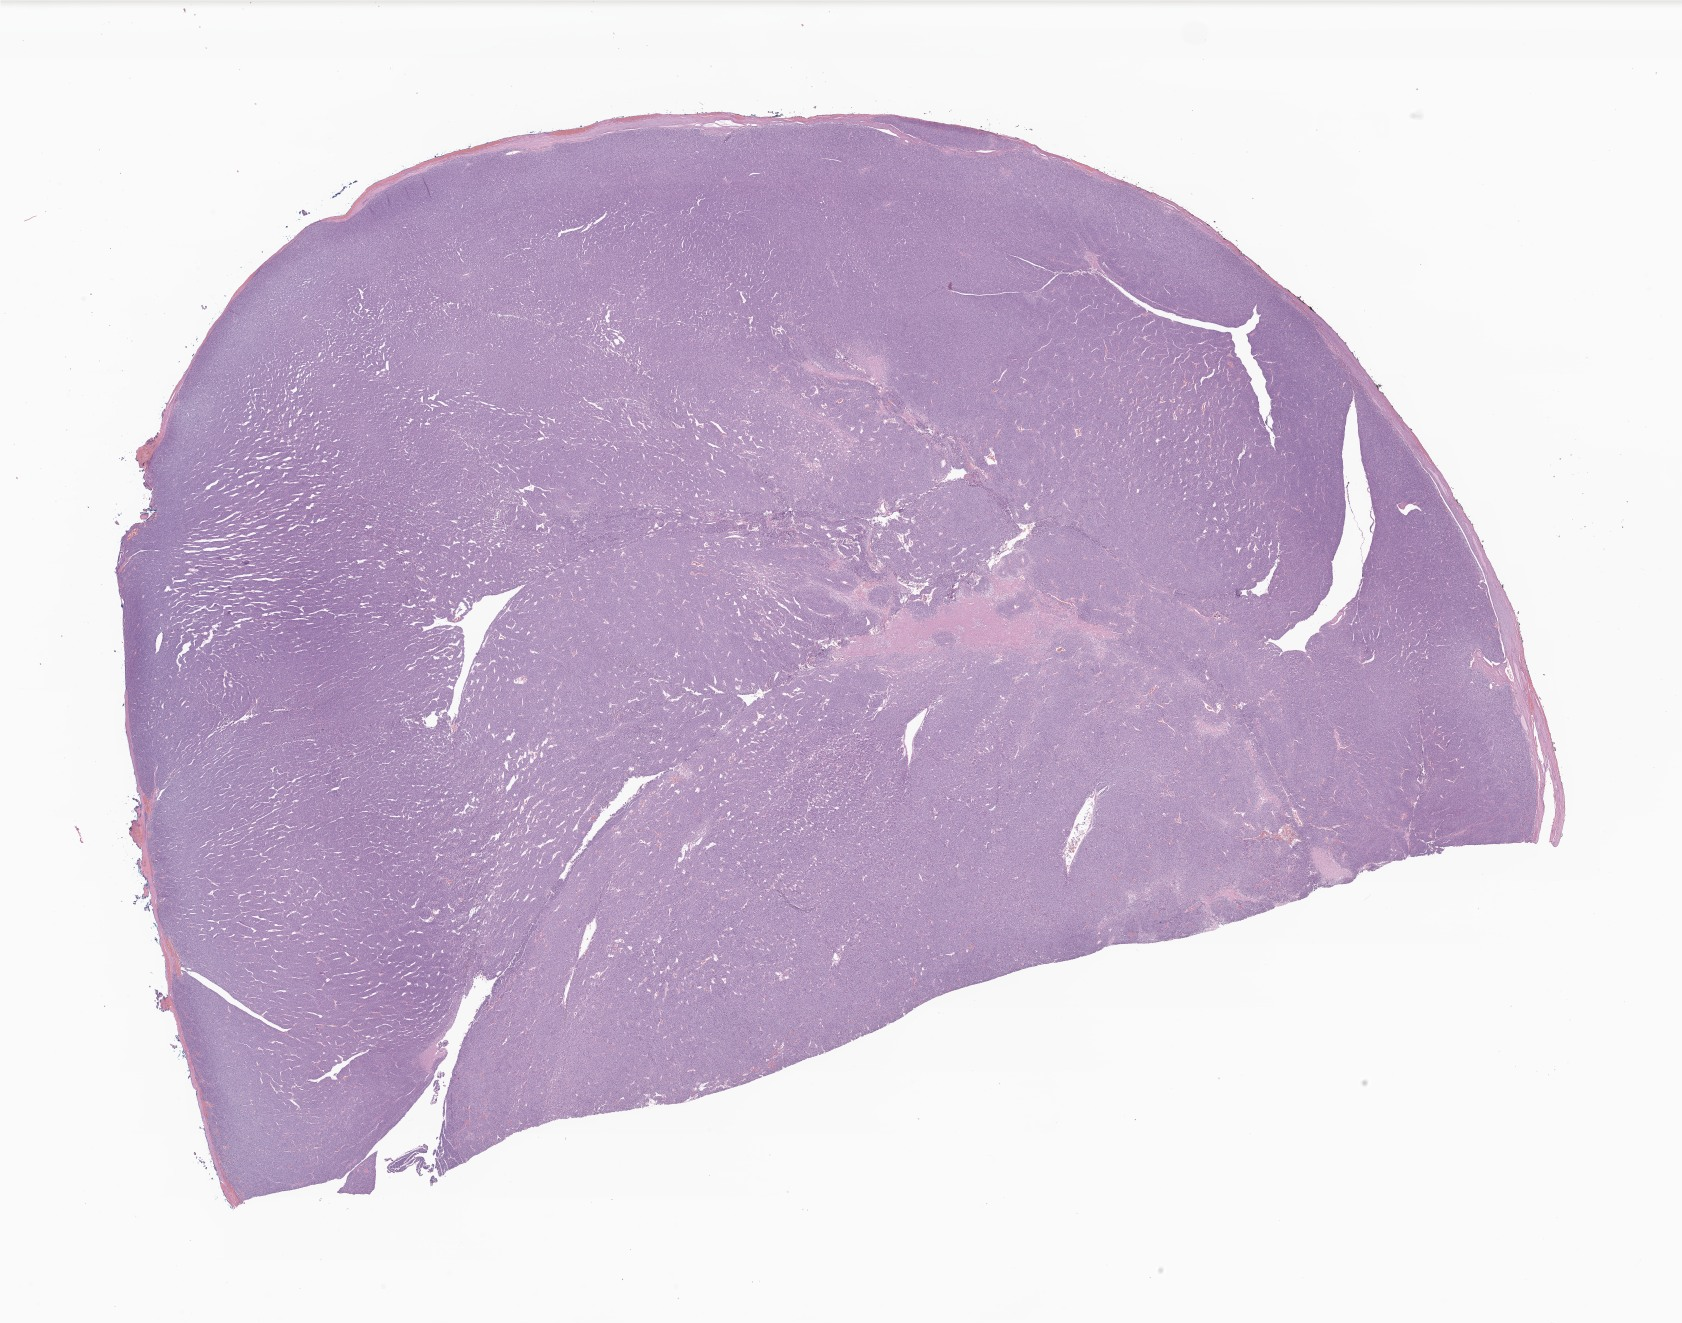
Digitized hematoxylin and eosin (H&E)-stained section of tumor tissue from the thyroid — whole scanned area (about 28.4 x 22.3 mm) shown as a low-resolution overview; FFPE section. Female patient, age 166 months (13 years 10 months).
Diagnosis: Follicular carcinoma, minimally invasive.